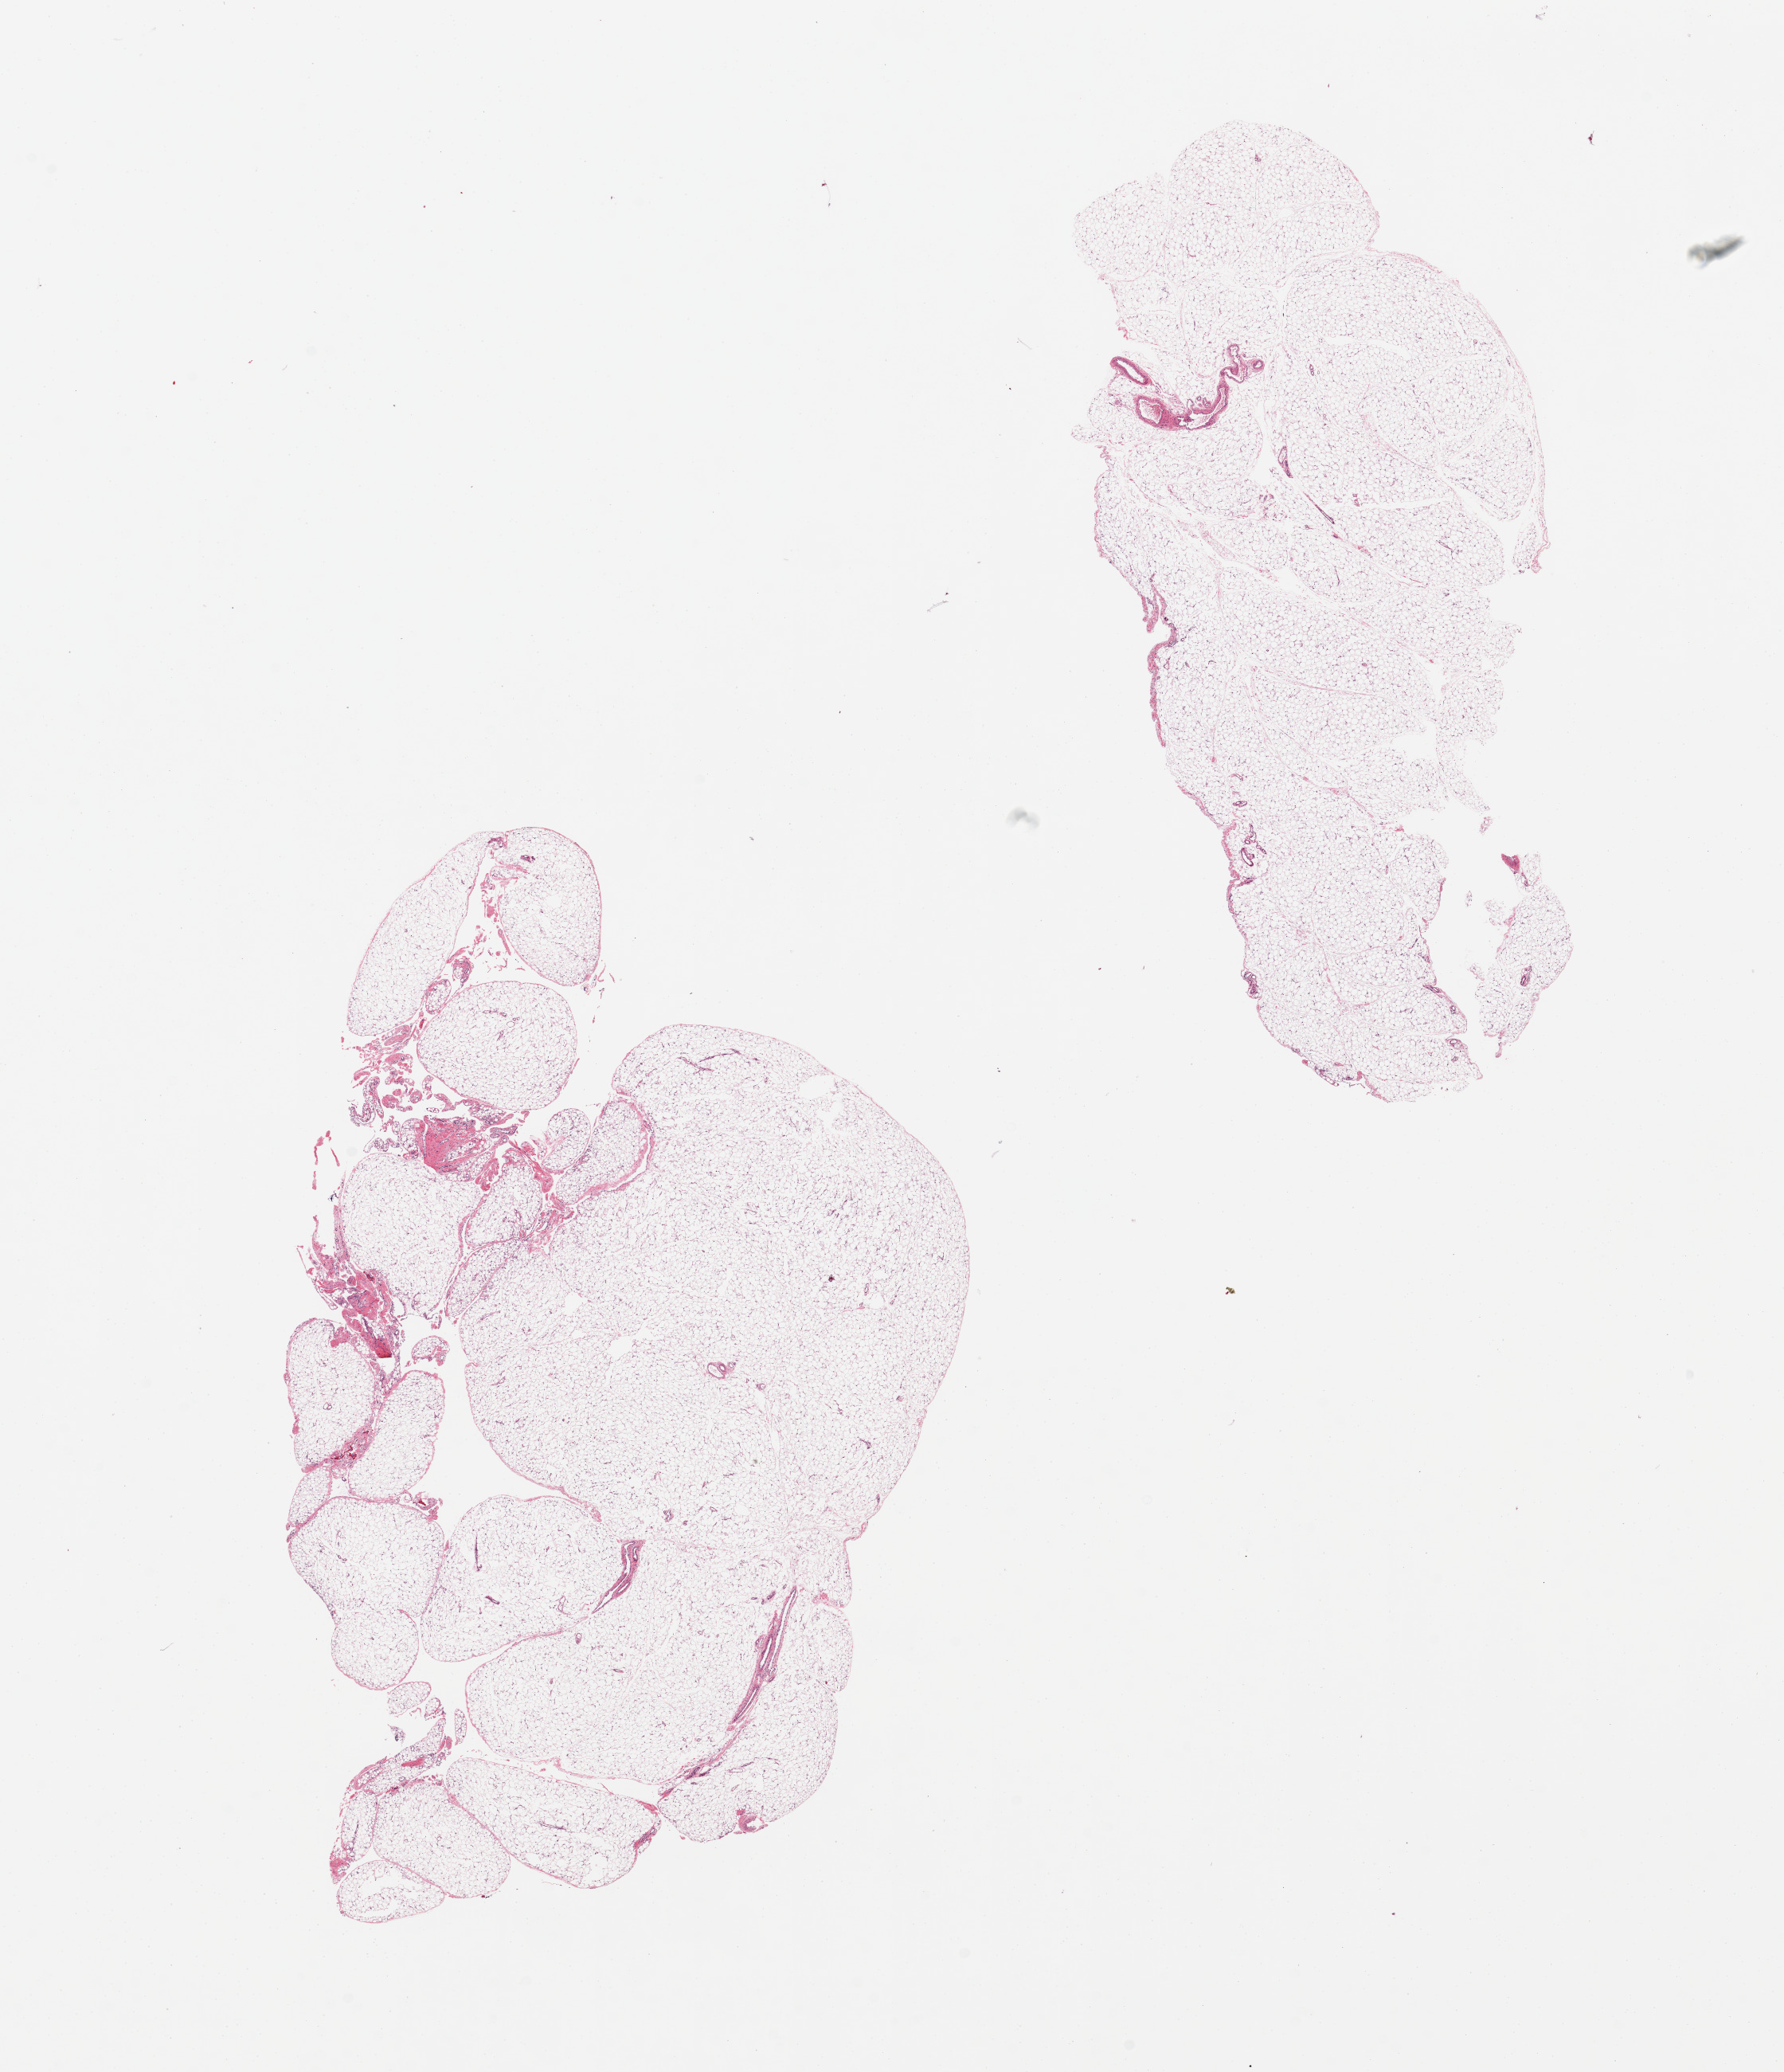
Whole-slide image, H&E stain — low-resolution overview of the scanned area, about 17.7 x 20.6 mm (from a 20x scan); PAXgene-fixed paraffin-embedded (PFPE) section; section of omentum (target tissue); tissue donor sample. Donor sex: female.
Review note (as recorded): 2 pieces.